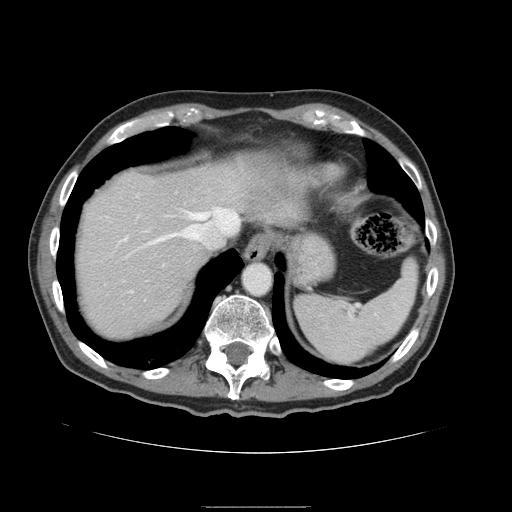
Contrast-enhanced abdominal CT, one axial slice. Slice 127 of 168 in the series (ordered by position). 120 kVp. Intravenous contrast given. Soft-tissue window (W 400 / L 40 HU). 2.5 mm slice thickness. 512 × 512 image matrix, field of view 386 × 386 mm. Male patient, age 74 years. Case-level facts recorded for this patient, not image findings: diagnosis: colorectal cancer liver metastases, imaged before liver resection; multiple liver metastases: no; largest metastasis: 14.5 cm; chemotherapy before resection: no.
Outlined on this slice (outlined manually by an expert reader):
- hepatic veins: box from (x=145, y=208) to (x=238, y=246) px
- liver: (x=74, y=157)–(x=297, y=341)
- planned liver remnant (the part of the liver to remain after resection): (x=75, y=157)–(x=295, y=341)